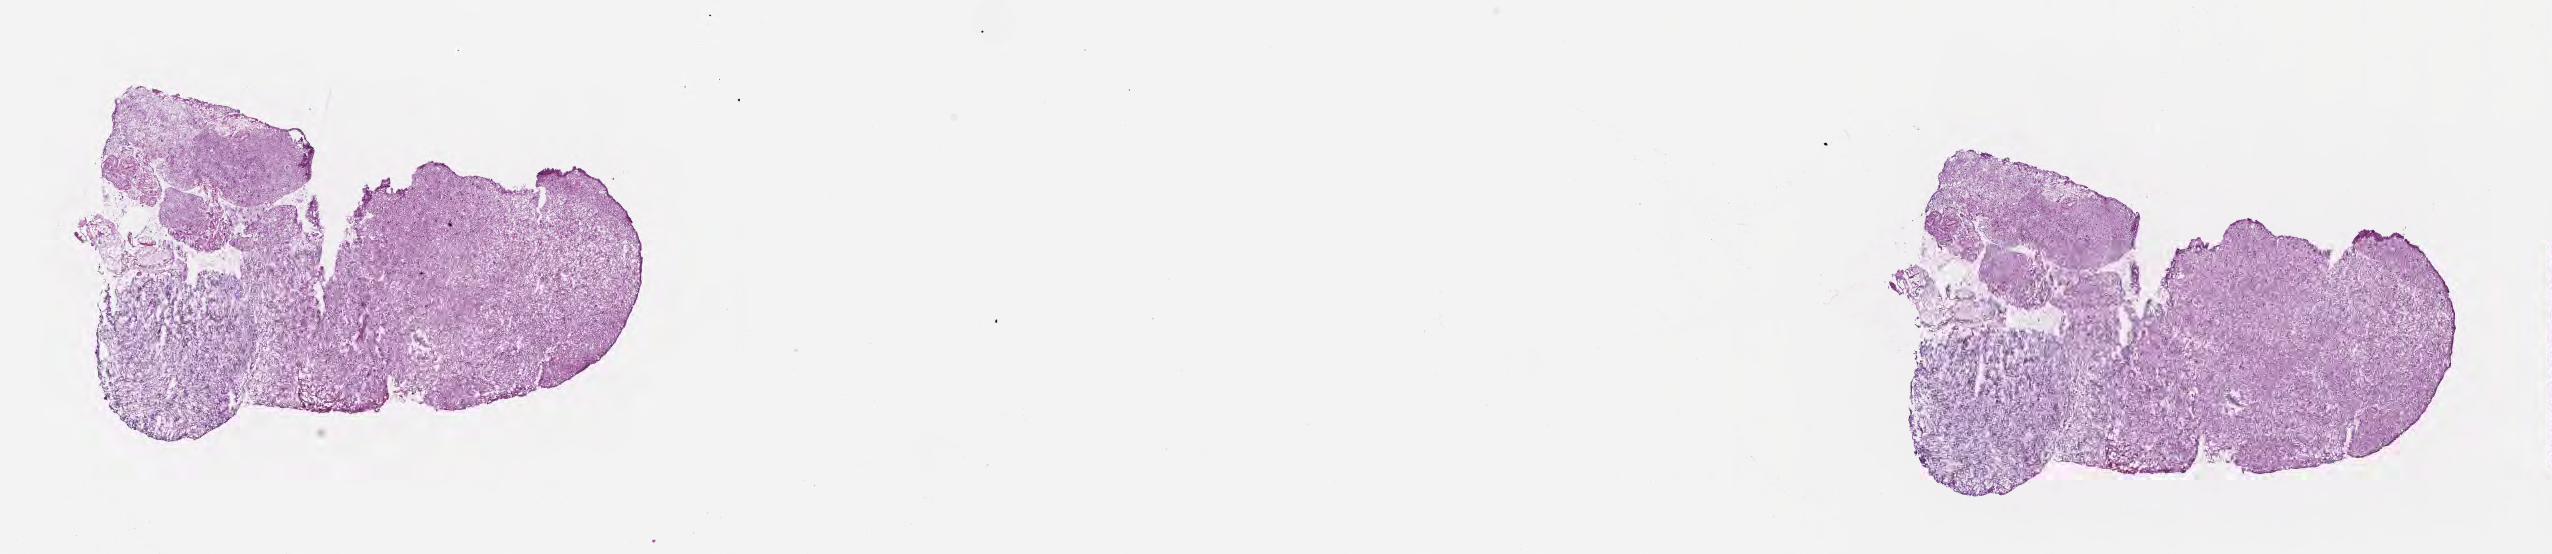
Haematoxylin and eosin whole-slide image — whole scanned area (about 20.6 x 4.5 mm) shown as a low-resolution overview, frozen section, primary tumor, anatomic site: brain. Female, age 58 years at initial diagnosis. Composition of this section per pathologist review: tumor cells 75%, tumor nuclei 92%, stromal cells 19%, necrosis 0%, normal cells 6%. Infiltration values recorded for this section: lymphocyte infiltration 0%, monocyte infiltration 0%, neutrophil infiltration 0%.
Diagnosis: Glioblastoma, NOS. Section: bottom of the tissue portion.